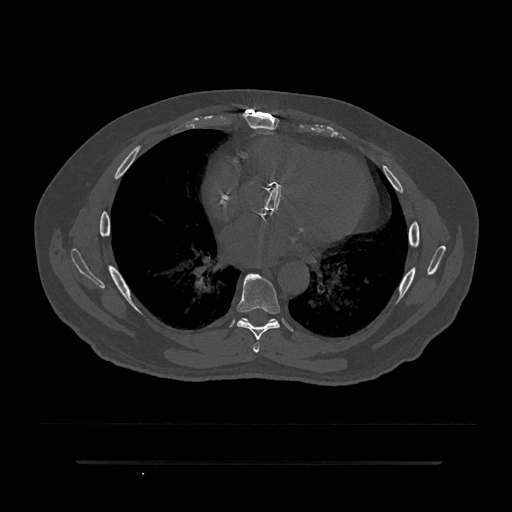
CT including the spine, one axial slice. Slice 470 of 797 in the series (ordered by position). Reconstruction kernel Br40s/3. Bone window (W 1800 / L 400 HU). 0.5 mm slice thickness. 512 × 512 image matrix. Patient: male, 59 years. From the clinical record (not read from this slice): primary cancer: bile ducts; vertebrae with lytic lesions (as recorded): T10.
Structures marked on this image (semi-automatic segmentation, software-assisted and operator-edited):
- T6 vertebra: bounding box (x1, y1, x2, y2) in pixels: (253, 342, 260, 353)
- T7 vertebra: (236, 273, 280, 340)
- T8 vertebra: (240, 318, 249, 322)